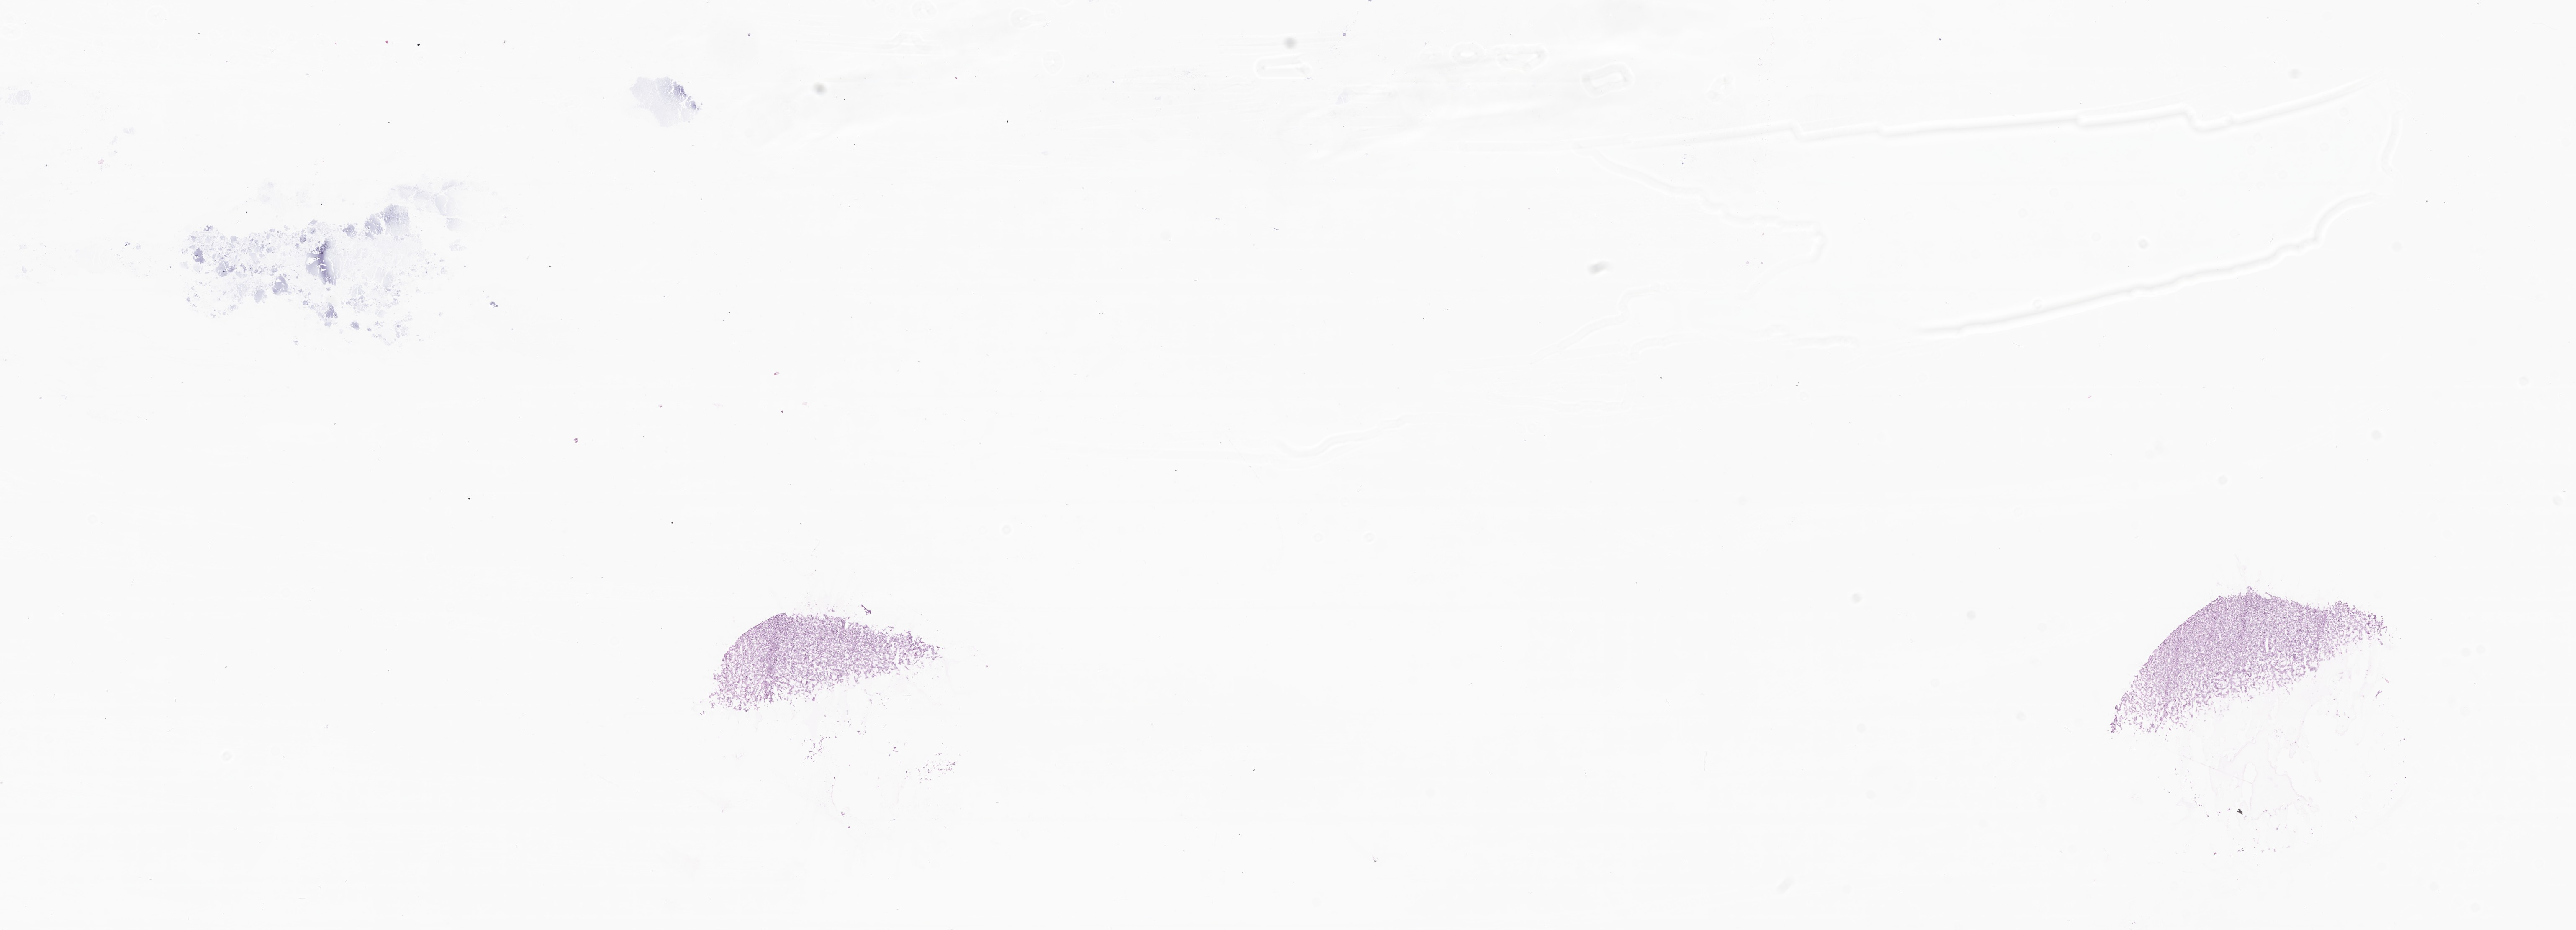
H&E whole-slide image, whole scanned area (about 25.9 x 9.4 mm) shown as a low-resolution overview. Frozen section. Metastatic tumor tissue, resected from peritoneum. Female patient; age at initial diagnosis 72 years. Composition of this section per pathologist review: tumor cells 90%, tumor nuclei 90%.
Patient diagnosis (primary): Adenocarcinoma, metastatic, NOS.